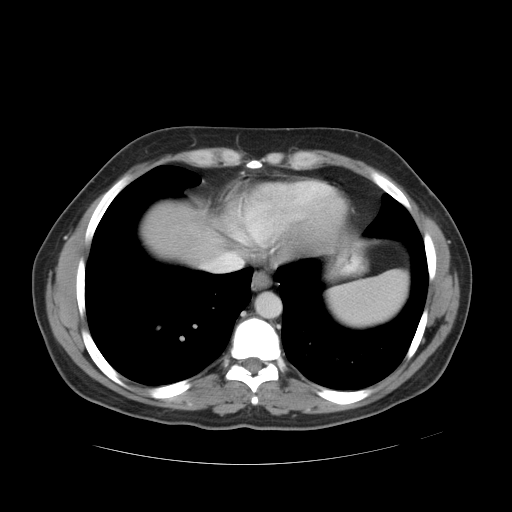
Contrast-enhanced abdominal CT, one axial slice. Slice 46 of 49 in the series (ordered by position). Reconstruction kernel STANDARD. Intravenous contrast given. Soft-tissue window (W 400 / L 40 HU). 512 × 512 image matrix, field of view 422 × 422 mm. Male patient, age 42 years. Case-level facts recorded for this patient, not image findings: diagnosis: colorectal cancer liver metastases, imaged before liver resection; multiple liver metastases: yes; largest metastasis: 2.8 cm; chemotherapy before resection: yes.
Annotated regions visible in this slice (manually delineated by an expert):
- hepatic veins: bounding box <201,251,236,267> (left, top, right, bottom; pixels)
- liver: <145,205,222,261>
- planned liver remnant (the part of the liver to remain after resection): <145,205,222,261>